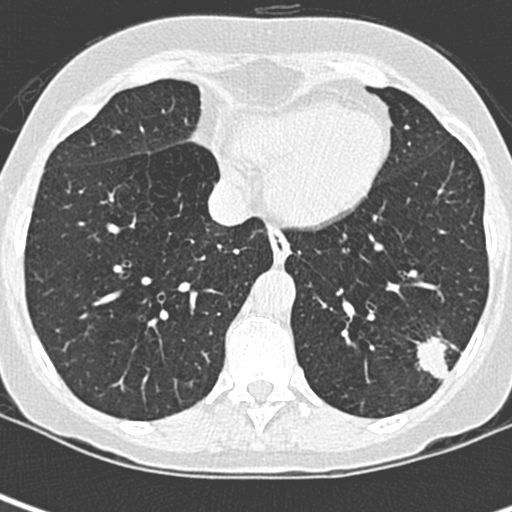
Low-dose screening chest CT, one axial slice; slice 90 of 252 in the series (ordered by position); lung window (W 1500 / L -600 HU); 512 × 512 image matrix.
Outlined on this slice (manually delineated by an expert):
- lesion 1 (tumor, lower lobe of left lung): bounding box [x1, y1, x2, y2] px = [416, 336, 448, 382]